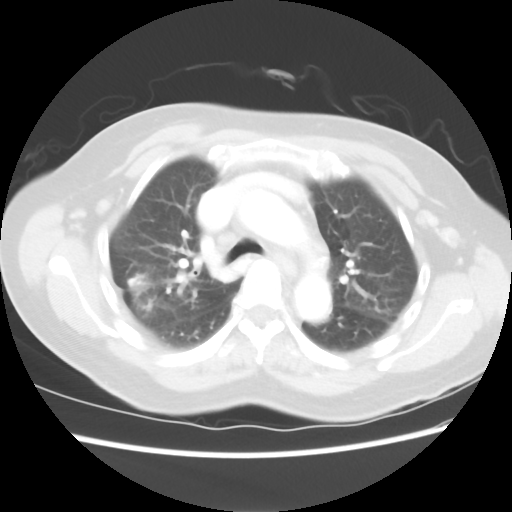
Chest CT, one axial slice; reconstruction kernel STANDARD; 100 kVp; lung window (W 1500 / L -600 HU); 5 mm slice thickness; 512 × 512 image matrix, field of view 342 × 342 mm. Female patient, age 67 years. From the clinical record (not read from this slice): clinical TNM (as recorded): T1c N1 M0.
Annotated regions visible in this slice (rectangle marked by the reading radiologist):
- lung tumour (recorded histology: adenocarcinoma): box from (x=127, y=264) to (x=165, y=325) px